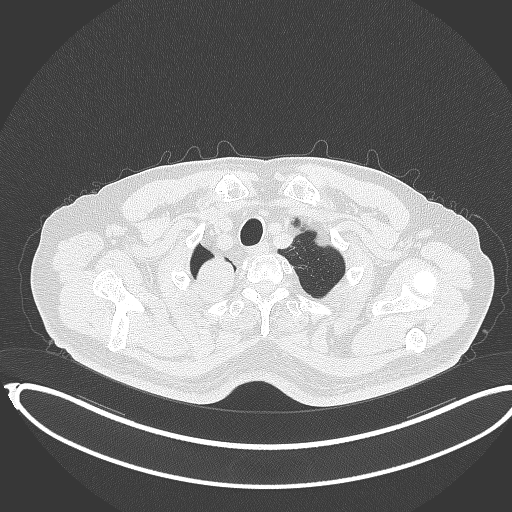
Chest CT, one axial slice; position 339 of 403 along the scan axis; reconstruction kernel B70f; lung window (W 1500 / L -600 HU); 1 mm slice thickness; 512 × 512 image matrix, field of view 436 × 436 mm. Patient: male, 68 years. Case-level facts recorded for this patient, not image findings: clinical TNM (as recorded): T2a N0 M0.
Annotated regions visible in this slice (rectangle marked by the reading radiologist):
- lung tumour (recorded histology: adenocarcinoma): bounding box [x1, y1, x2, y2] px = [195, 253, 239, 300]